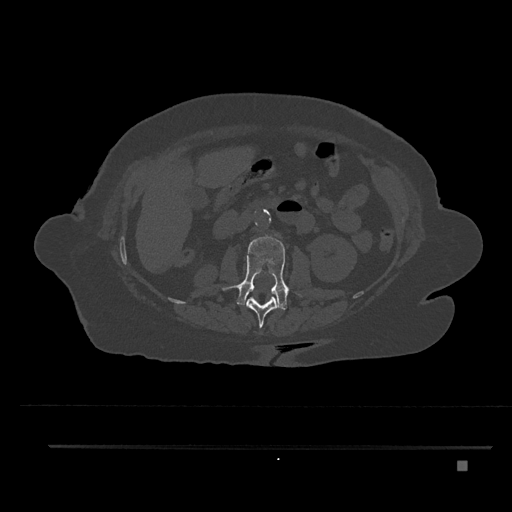
CT including the spine, one axial slice. Slice 189 of 797 in the series (ordered by position). Reconstruction kernel Br40s/3. Bone window (W 1800 / L 400 HU). 0.5 mm slice thickness. 512 × 512 image matrix, field of view 437 × 437 mm. Female patient, age 76 years. From the clinical record (not read from this slice): primary cancer: lung; vertebrae with lytic lesions (as recorded): T11, L3.
Outlined on this slice (semi-automatically segmented with operator editing):
- L1 vertebra: bounding box [x1, y1, x2, y2] px = [246, 296, 278, 328]
- L2 vertebra: [223, 235, 289, 310]